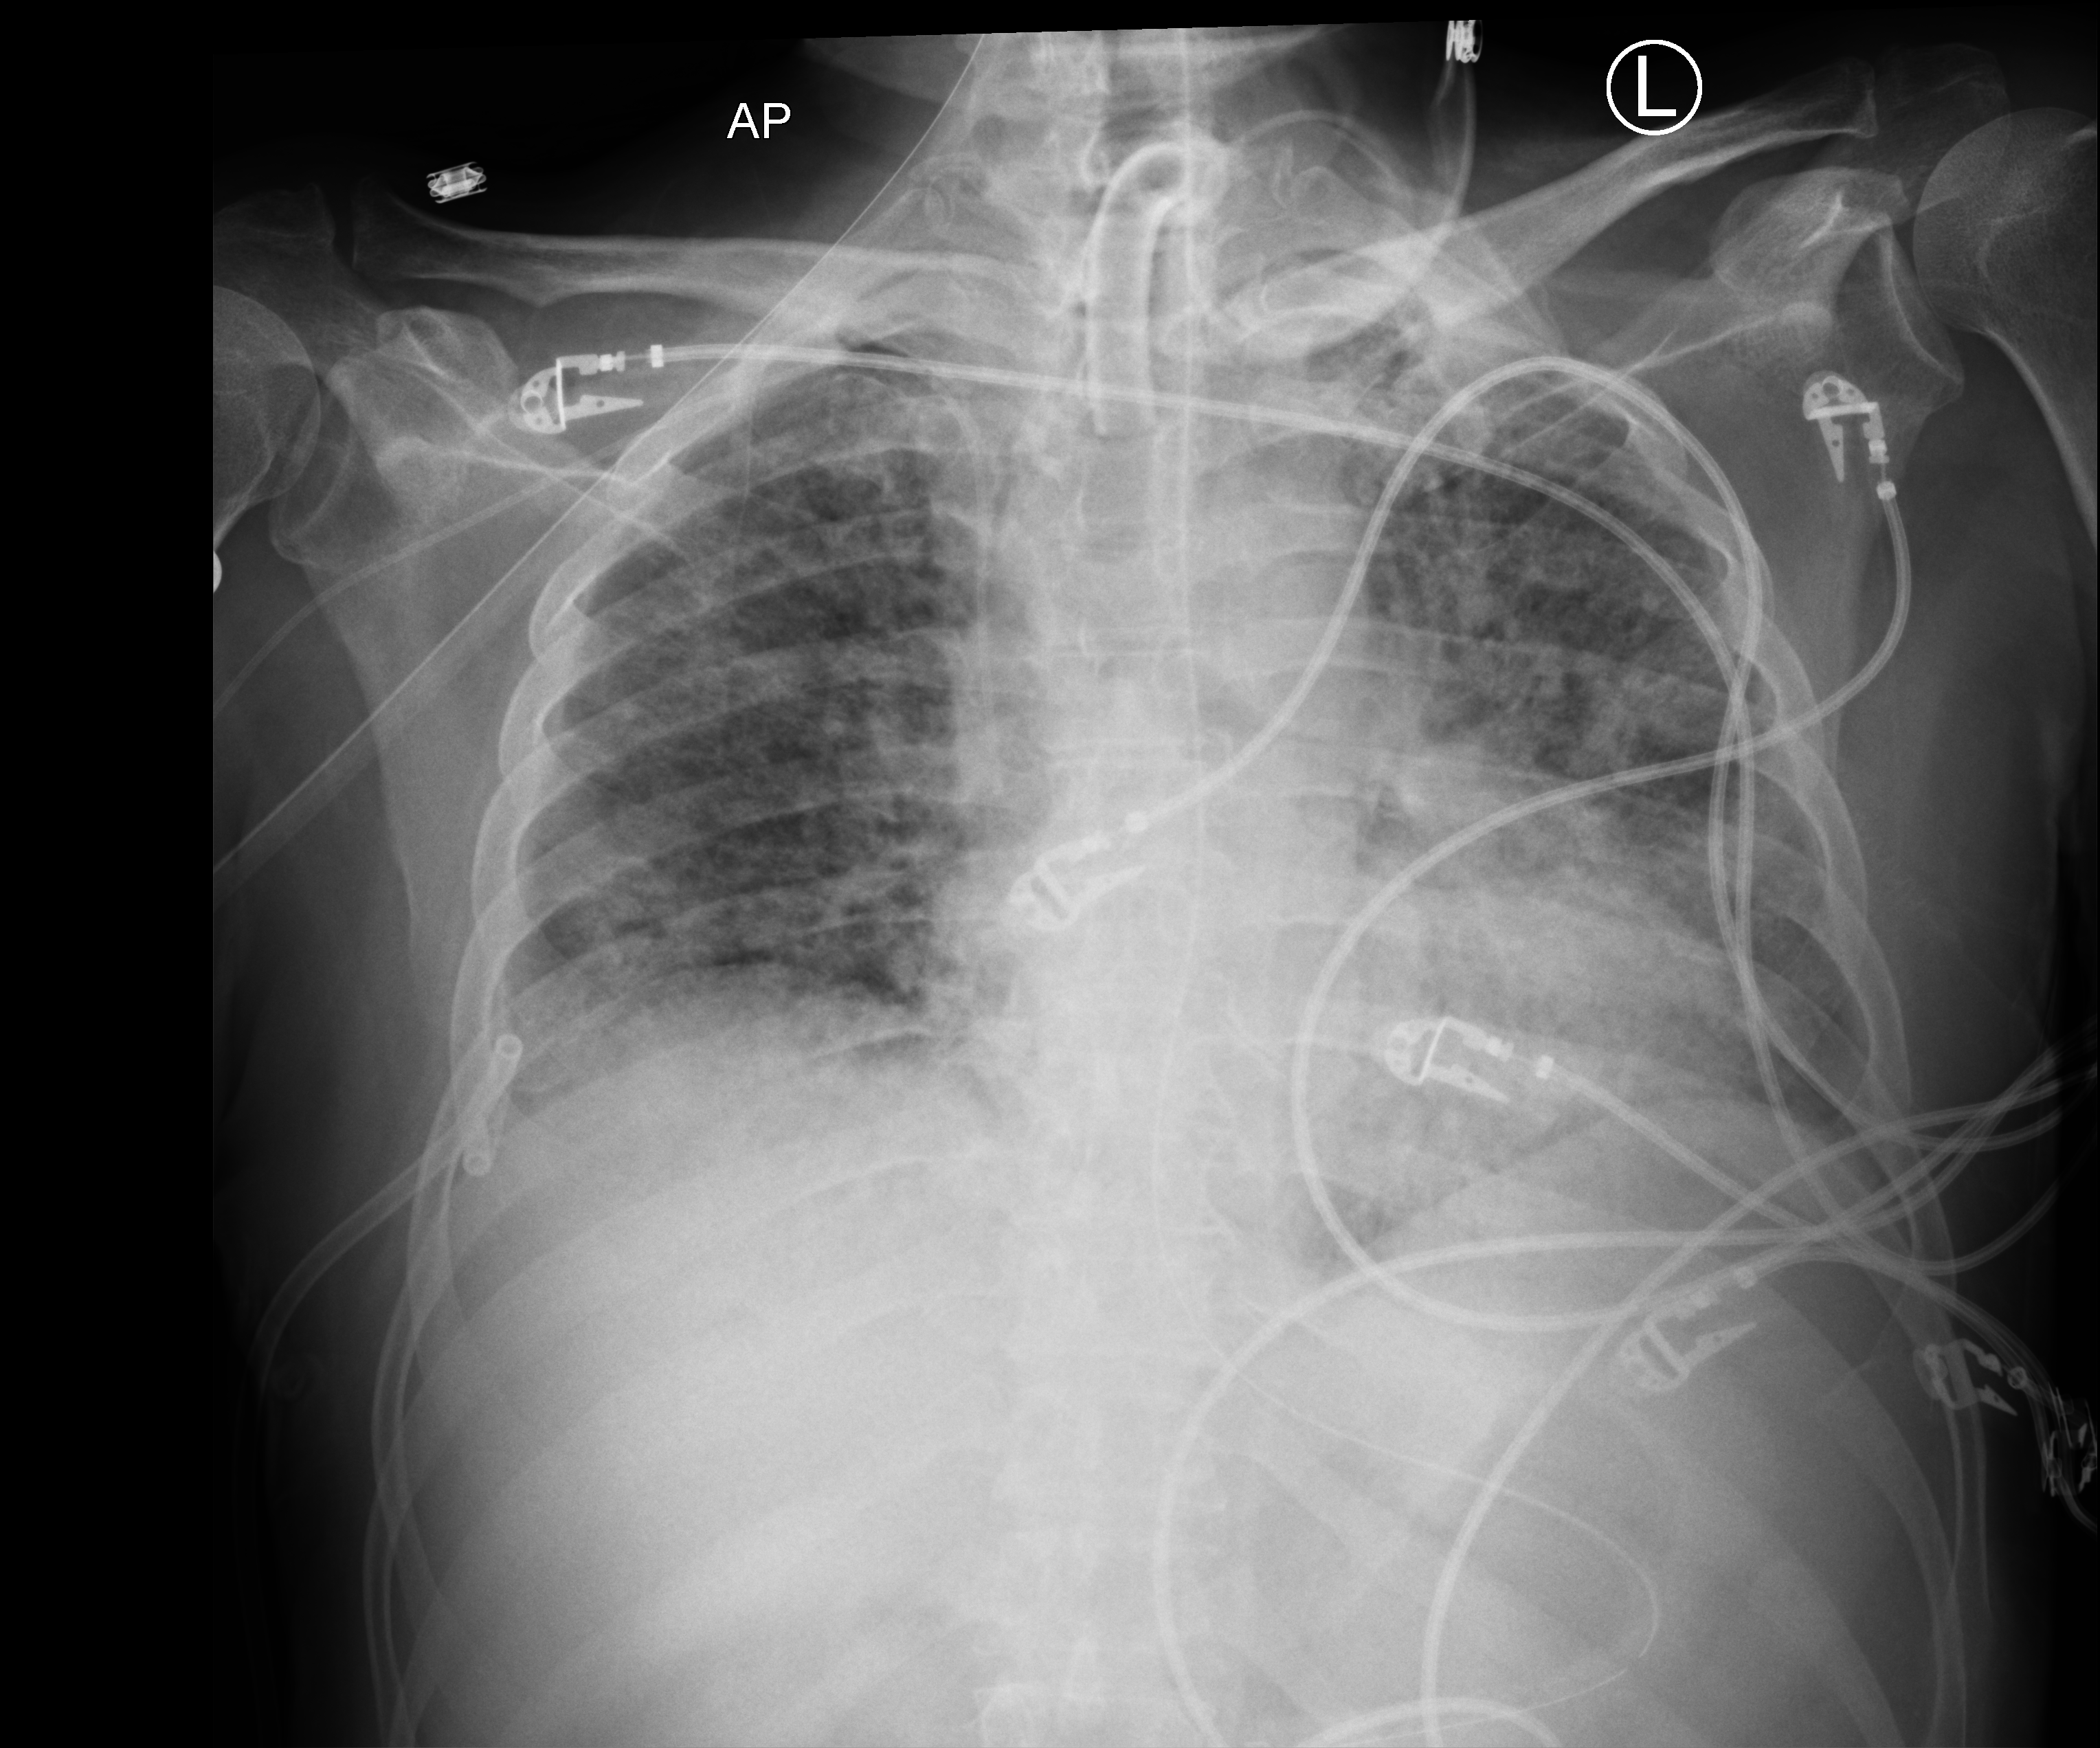
Chest X-ray (portable); anteroposterior (AP) projection. Male patient hospitalised with COVID-19, age 18–59 years.
From the hospital-stay record, not from the radiograph (when in the stay this image was taken is not recorded):
- length of hospital stay: 77 days
- diabetes (admission record): no
- hypertension (admission record): no